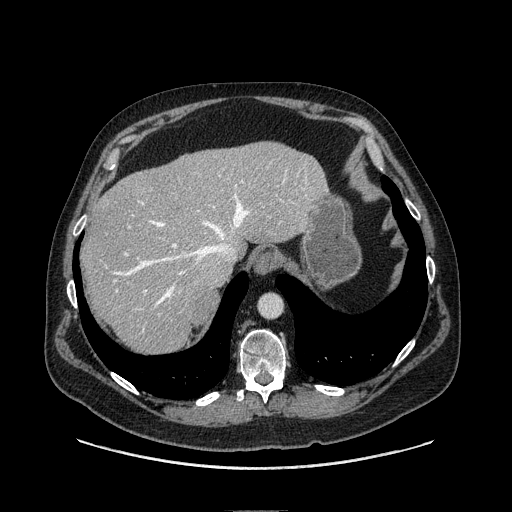
Contrast-enhanced abdominal CT, one axial slice. Soft-tissue window (W 400 / L 40 HU). 1.25 mm slice thickness. 512 × 512 image matrix. Male patient. From the clinical record (not read from this slice): diagnosis: adrenocortical carcinoma; tumour side: right adrenal; tumour size at pathology: 7.5 cm; Ki-67 index: 15 %.
Outlined on this slice (semi-automatically segmented with operator editing):
- mass: bounding box [x1, y1, x2, y2] px = [195, 292, 217, 323]